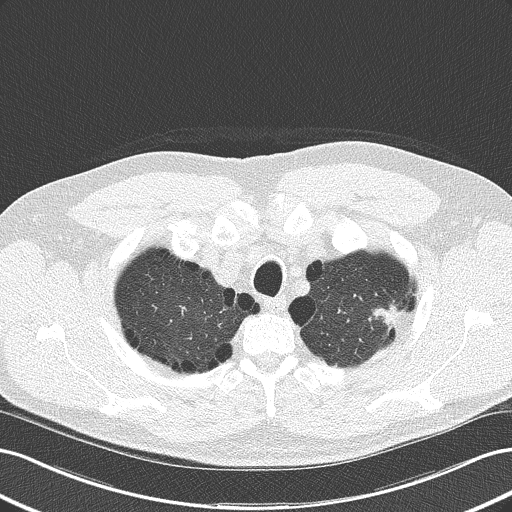
Low-dose screening chest CT, axial slice, second annual screen, lung window (W 1500 / L -600 HU), 2 mm slice thickness. Male, age 62 years at enrolment. Current smoker at enrolment.
Expert-annotated lung lesion, bounding box <356,289,413,338> (left, top, right, bottom; pixels). The screening reader recorded 2 non-calcified nodules or masses ≥4 mm on this exam (left upper lobe, right middle lobe); which of them this box marks is not recorded. Official screen result: positive, other. Lung cancer was diagnosed 46 days after this screen: adenocarcinoma, NOS, left upper lobe, well differentiated (G1), stage IB (AJCC 6th edition), 17 mm at pathology.